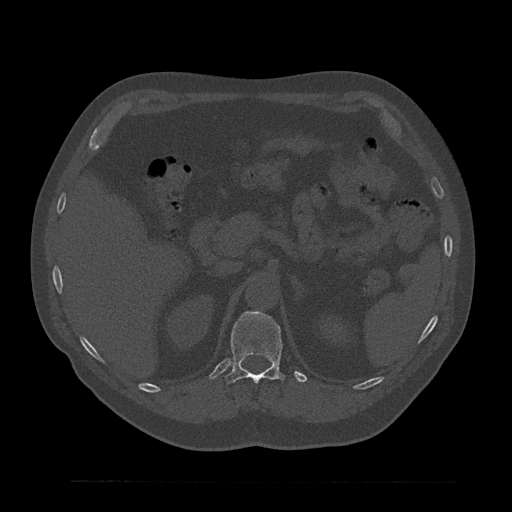
CT including the spine, one axial slice. Reconstruction kernel Br40s/3. Bone window (W 1800 / L 400 HU). 0.5 mm slice thickness. 512 × 512 image matrix, field of view 430 × 430 mm. Patient: male, 61 years. Case-level facts recorded for this patient, not image findings: primary cancer: prostate.
Structures marked on this image (semi-automatically segmented with operator editing):
- T12 vertebra: bounding box <225,312,286,384> (left, top, right, bottom; pixels)